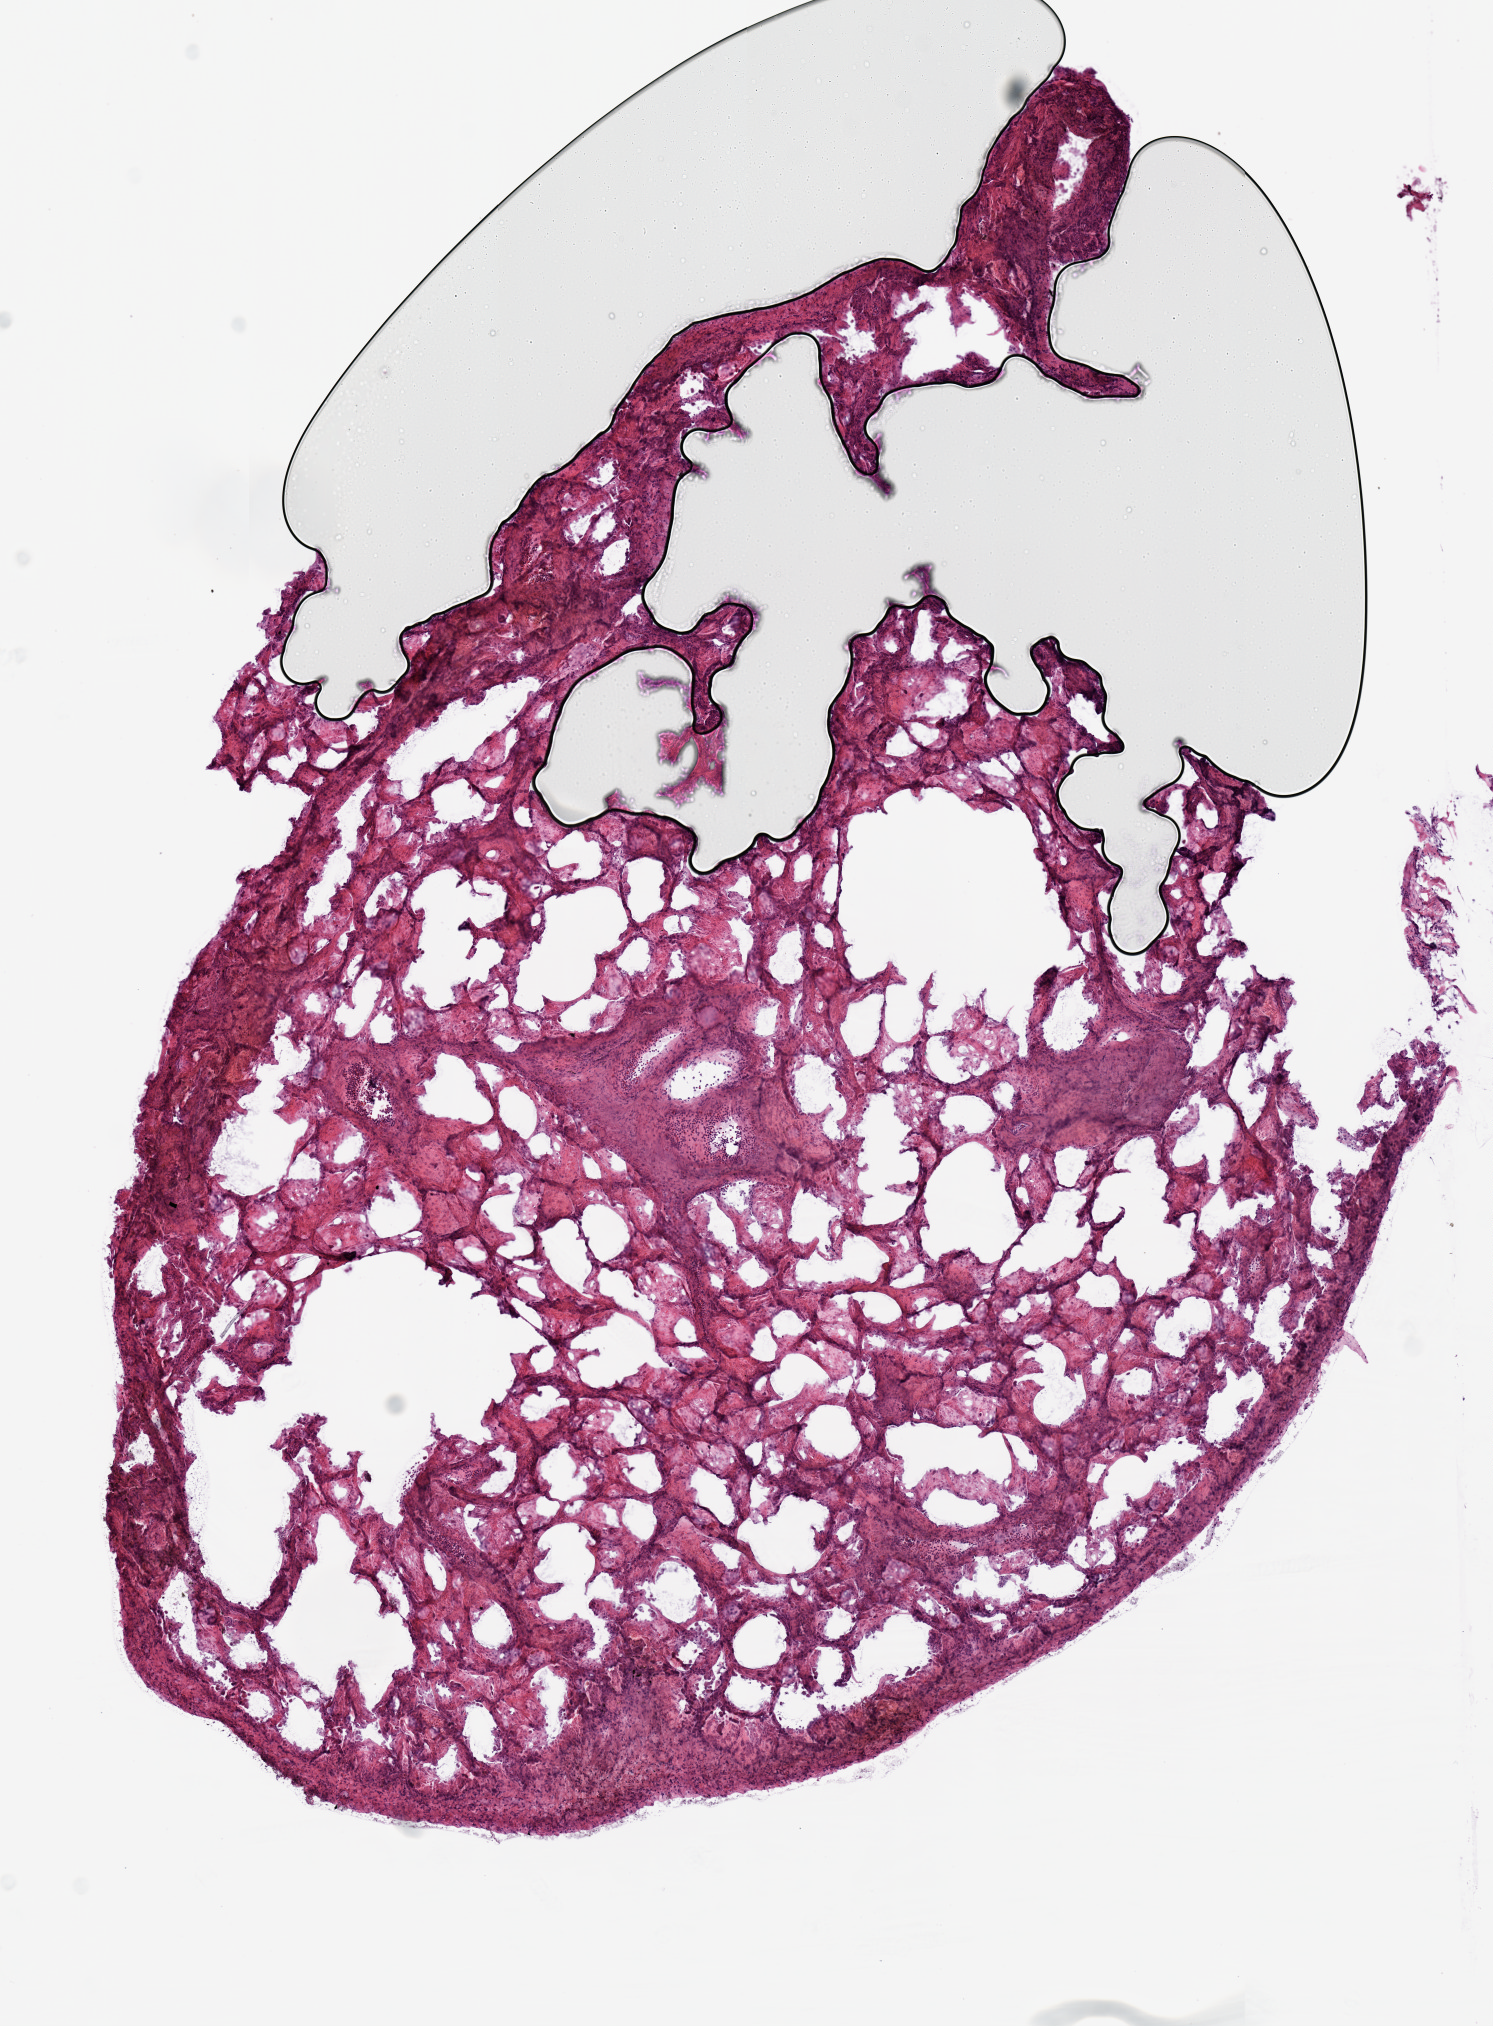
Whole-slide histology image, Hematoxylin and eosin (H&E) stained — low-resolution overview of the scanned area, about 5.9 x 8.0 mm (slide scanned at 20x). Frozen section from the top of the tissue portion. Sample: solid tissue normal (non-tumour tissue), lung. Patient: male, age at initial diagnosis 61 years.
* this section: solid tissue normal sample (biorepository sample class)
* patient diagnosis: Adenocarcinoma with mixed subtypes (lower lobe, lung)